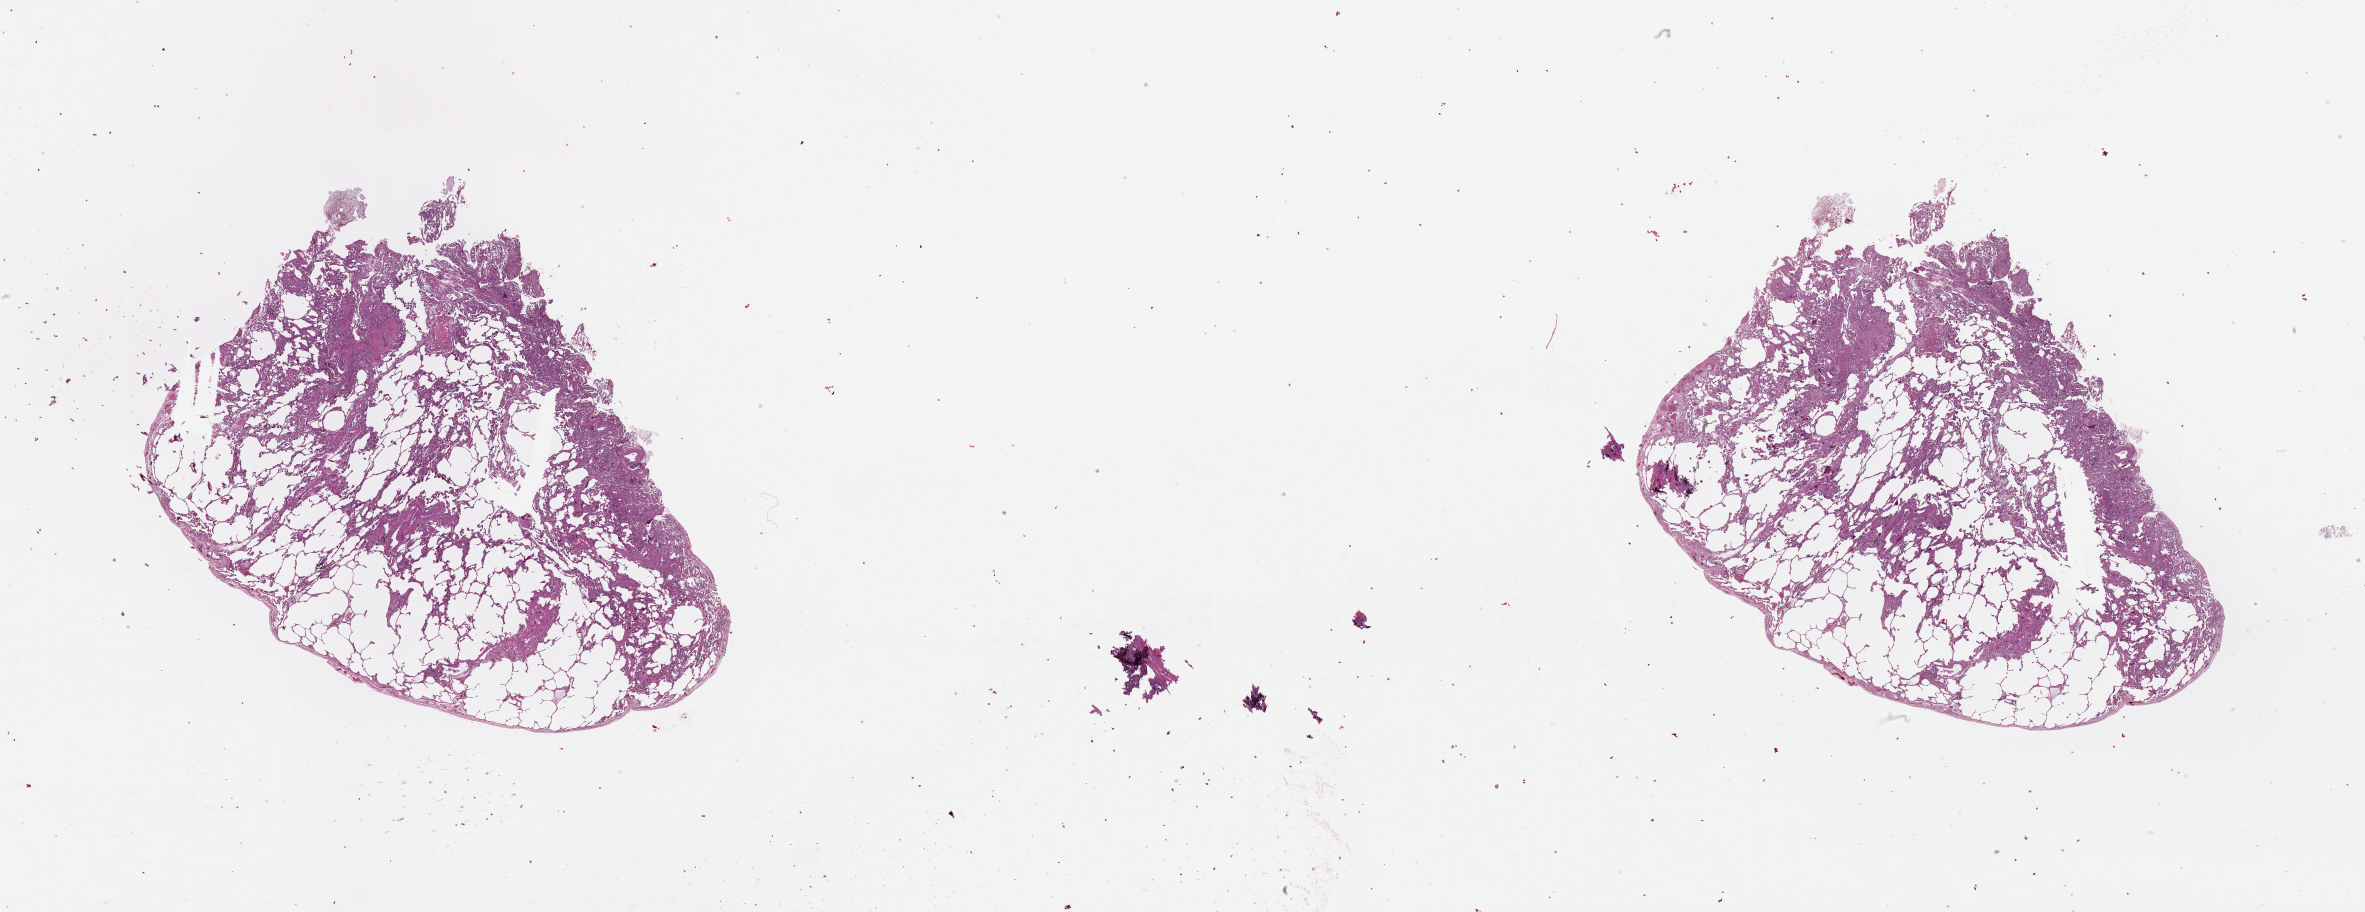
Digitized H&E tissue section (whole slide) — shown as a low-resolution overview of the whole scanned area (about 38.1 x 14.7 mm, from a 20x scan), normal (non-tumour) tissue sample, lung. Male, 65 y/o.
This section: normal (non-tumour) tissue from the same patient. Patient diagnosis (cohort enrolment): squamous cell carcinoma (lung).